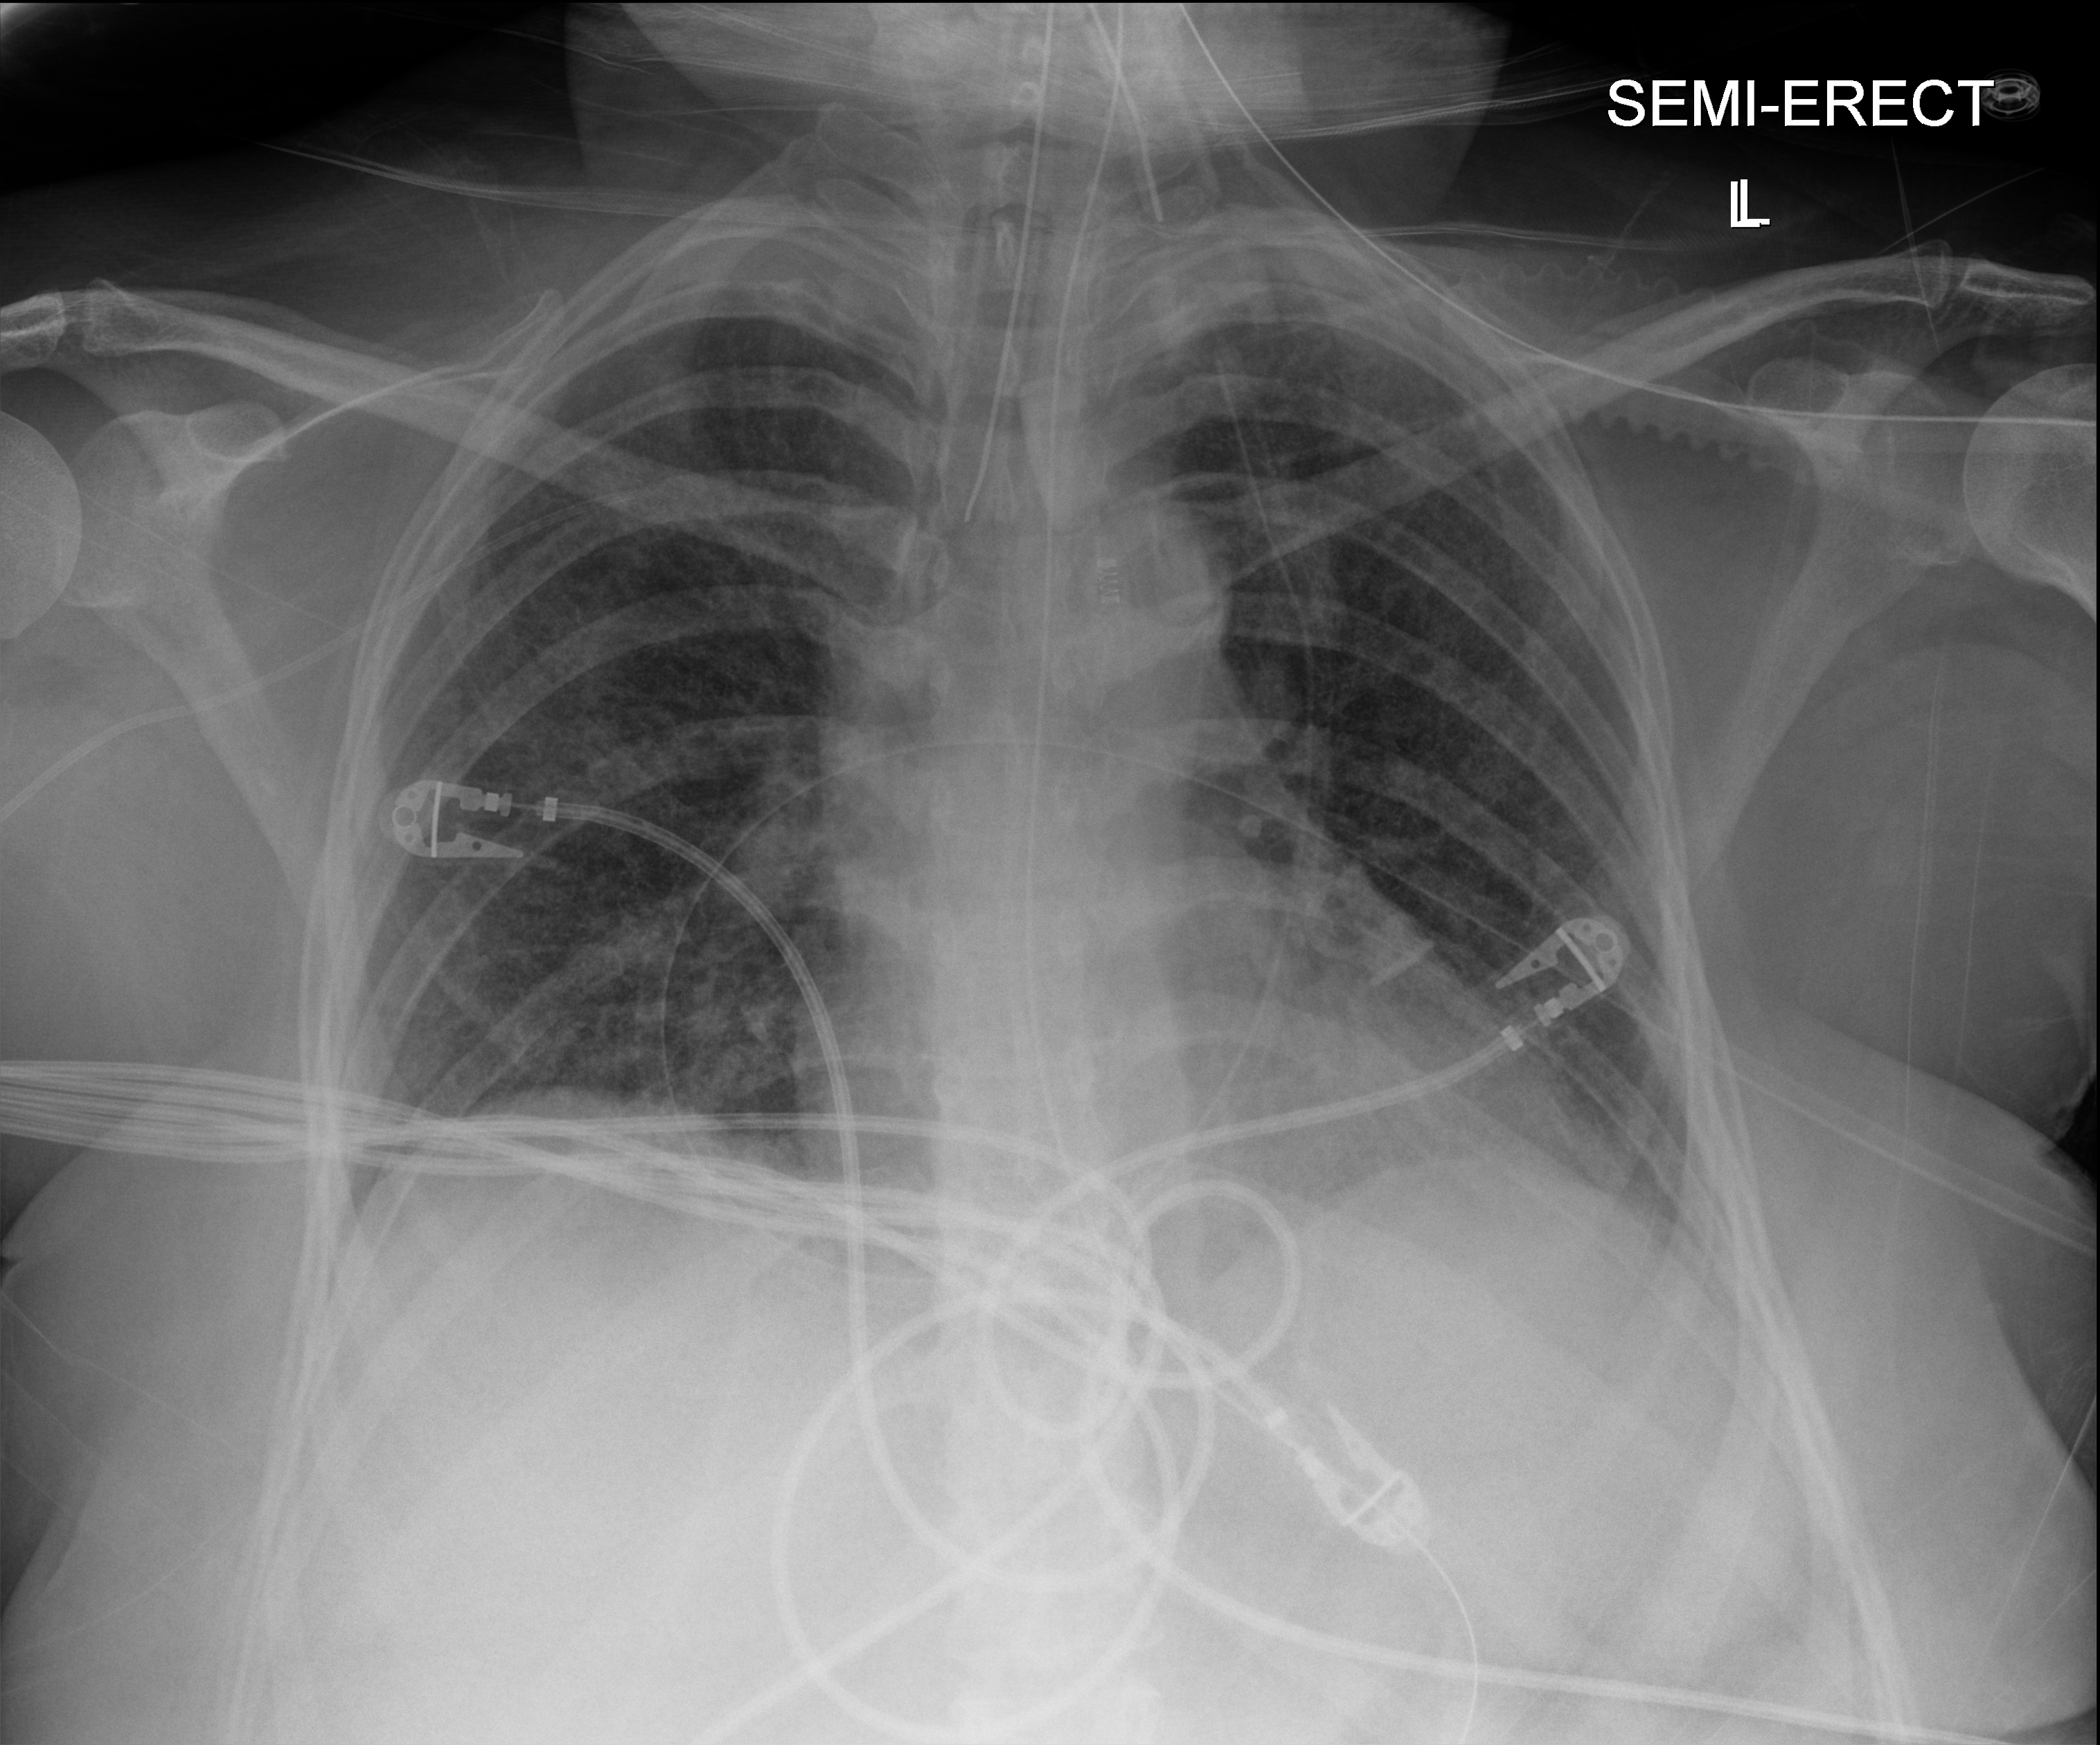
Bedside chest radiograph (digital radiography). Patient hospitalised with COVID-19; female, aged 18–59 years.
Admission-level facts for this patient (not findings on this image; timing relative to this image not recorded): admitted to intensive care during this hospital stay: yes.